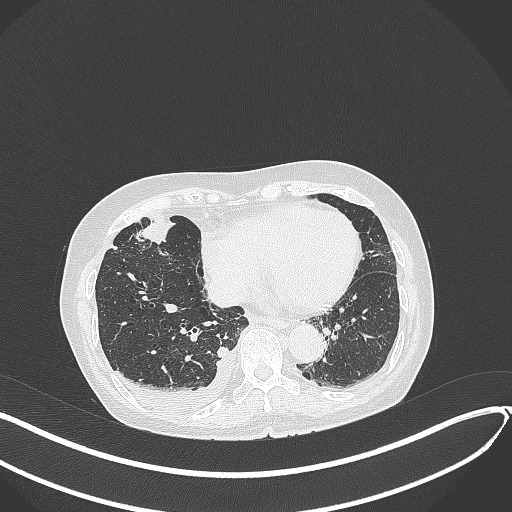
Chest CT, one axial slice. Position 123 of 418 along the scan axis. Reconstruction kernel B70f. Lung window (W 1500 / L -600 HU). 1 mm slice thickness. 512 × 512 image matrix. Patient: female, 75 years. From the clinical record (not read from this slice): clinical TNM (as recorded): T2a N3 M0.
Outlined on this slice (rectangle marked by the reading radiologist):
- lung tumour (recorded histology: adenocarcinoma): bounding box <137,215,182,252> (left, top, right, bottom; pixels)